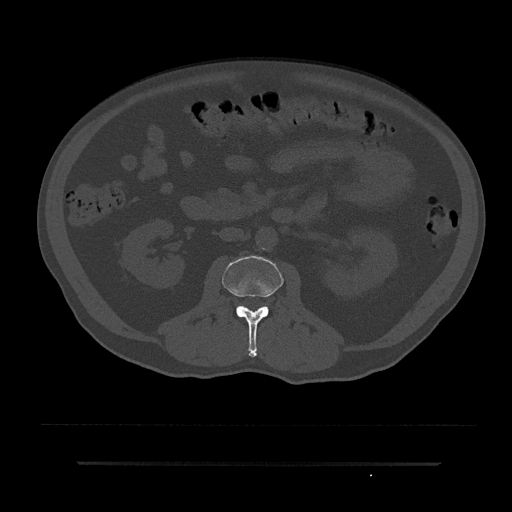
CT including the spine, one axial slice. Position 60 of 797 along the scan axis. Reconstruction kernel Br40s/3. Bone window (W 1800 / L 400 HU). 512 × 512 image matrix. Patient: male, 59 years. From the clinical record (not read from this slice): primary cancer: bile ducts; vertebrae with lytic lesions (as recorded): T10.
Structures marked on this image (semi-automatically segmented with operator editing):
- L2 vertebra: bounding box [x1, y1, x2, y2] px = [222, 256, 283, 357]